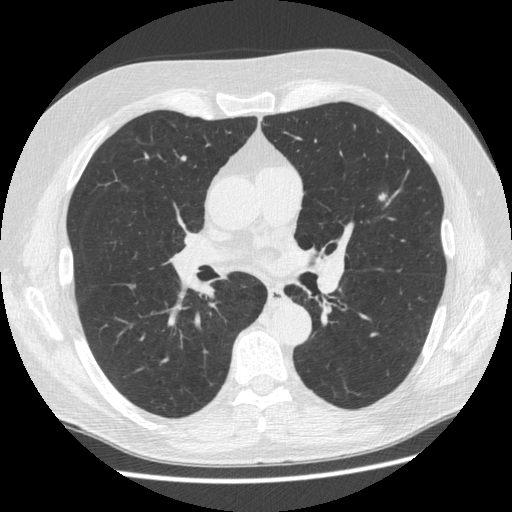
Low-dose screening chest CT, one axial slice; slice 303 of 545 in the series (ordered by position); 120 kVp; lung window (W 1500 / L -600 HU); 1.25 mm slice thickness; 512 × 512 image matrix.
Annotated regions visible in this slice (manually delineated by an expert):
- lesion 1 (nodule, upper lobe of left lung): bounding box [x1, y1, x2, y2] px = [379, 191, 388, 201]